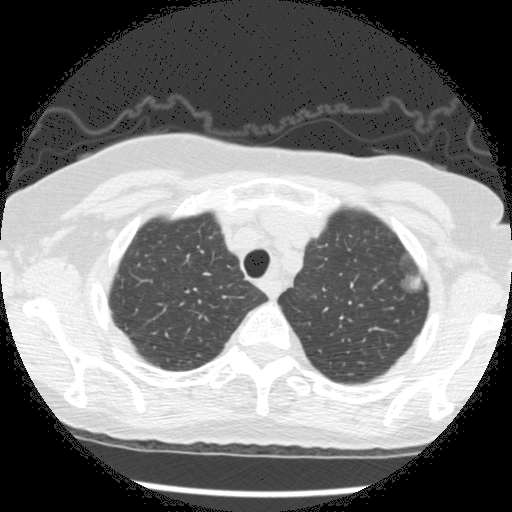
Low-dose screening chest CT, axial slice; second screening round (one year after baseline); lung window (W 1500 / L -600 HU); standard (soft-tissue) reconstruction kernel (STANDARD); slice 35 of 266 in the series; 512 × 512 image matrix, field of view 320 × 320 mm. Female, age 73 years at enrolment. Former smoker at enrolment.
Expert-annotated lung lesion, bounding box (x1, y1, x2, y2) in pixels: (386, 251, 431, 297). The screening reader recorded 3 non-calcified nodules or masses ≥4 mm on this exam (left upper lobe, left upper lobe, left upper lobe); which of them this box marks is not recorded. Official screen result: positive, change unspecified: nodule(s) >= 4 mm or enlarging nodule(s), mass(es), or other non-specific abnormalities suspicious for lung cancer. Participant outcome: lung cancer diagnosed 49 days after this screen — bronchiolo-alveolar adenocarcinoma, NOS, left upper lobe, well differentiated (G1), stage IA (AJCC 6th edition), 10 mm at pathology.